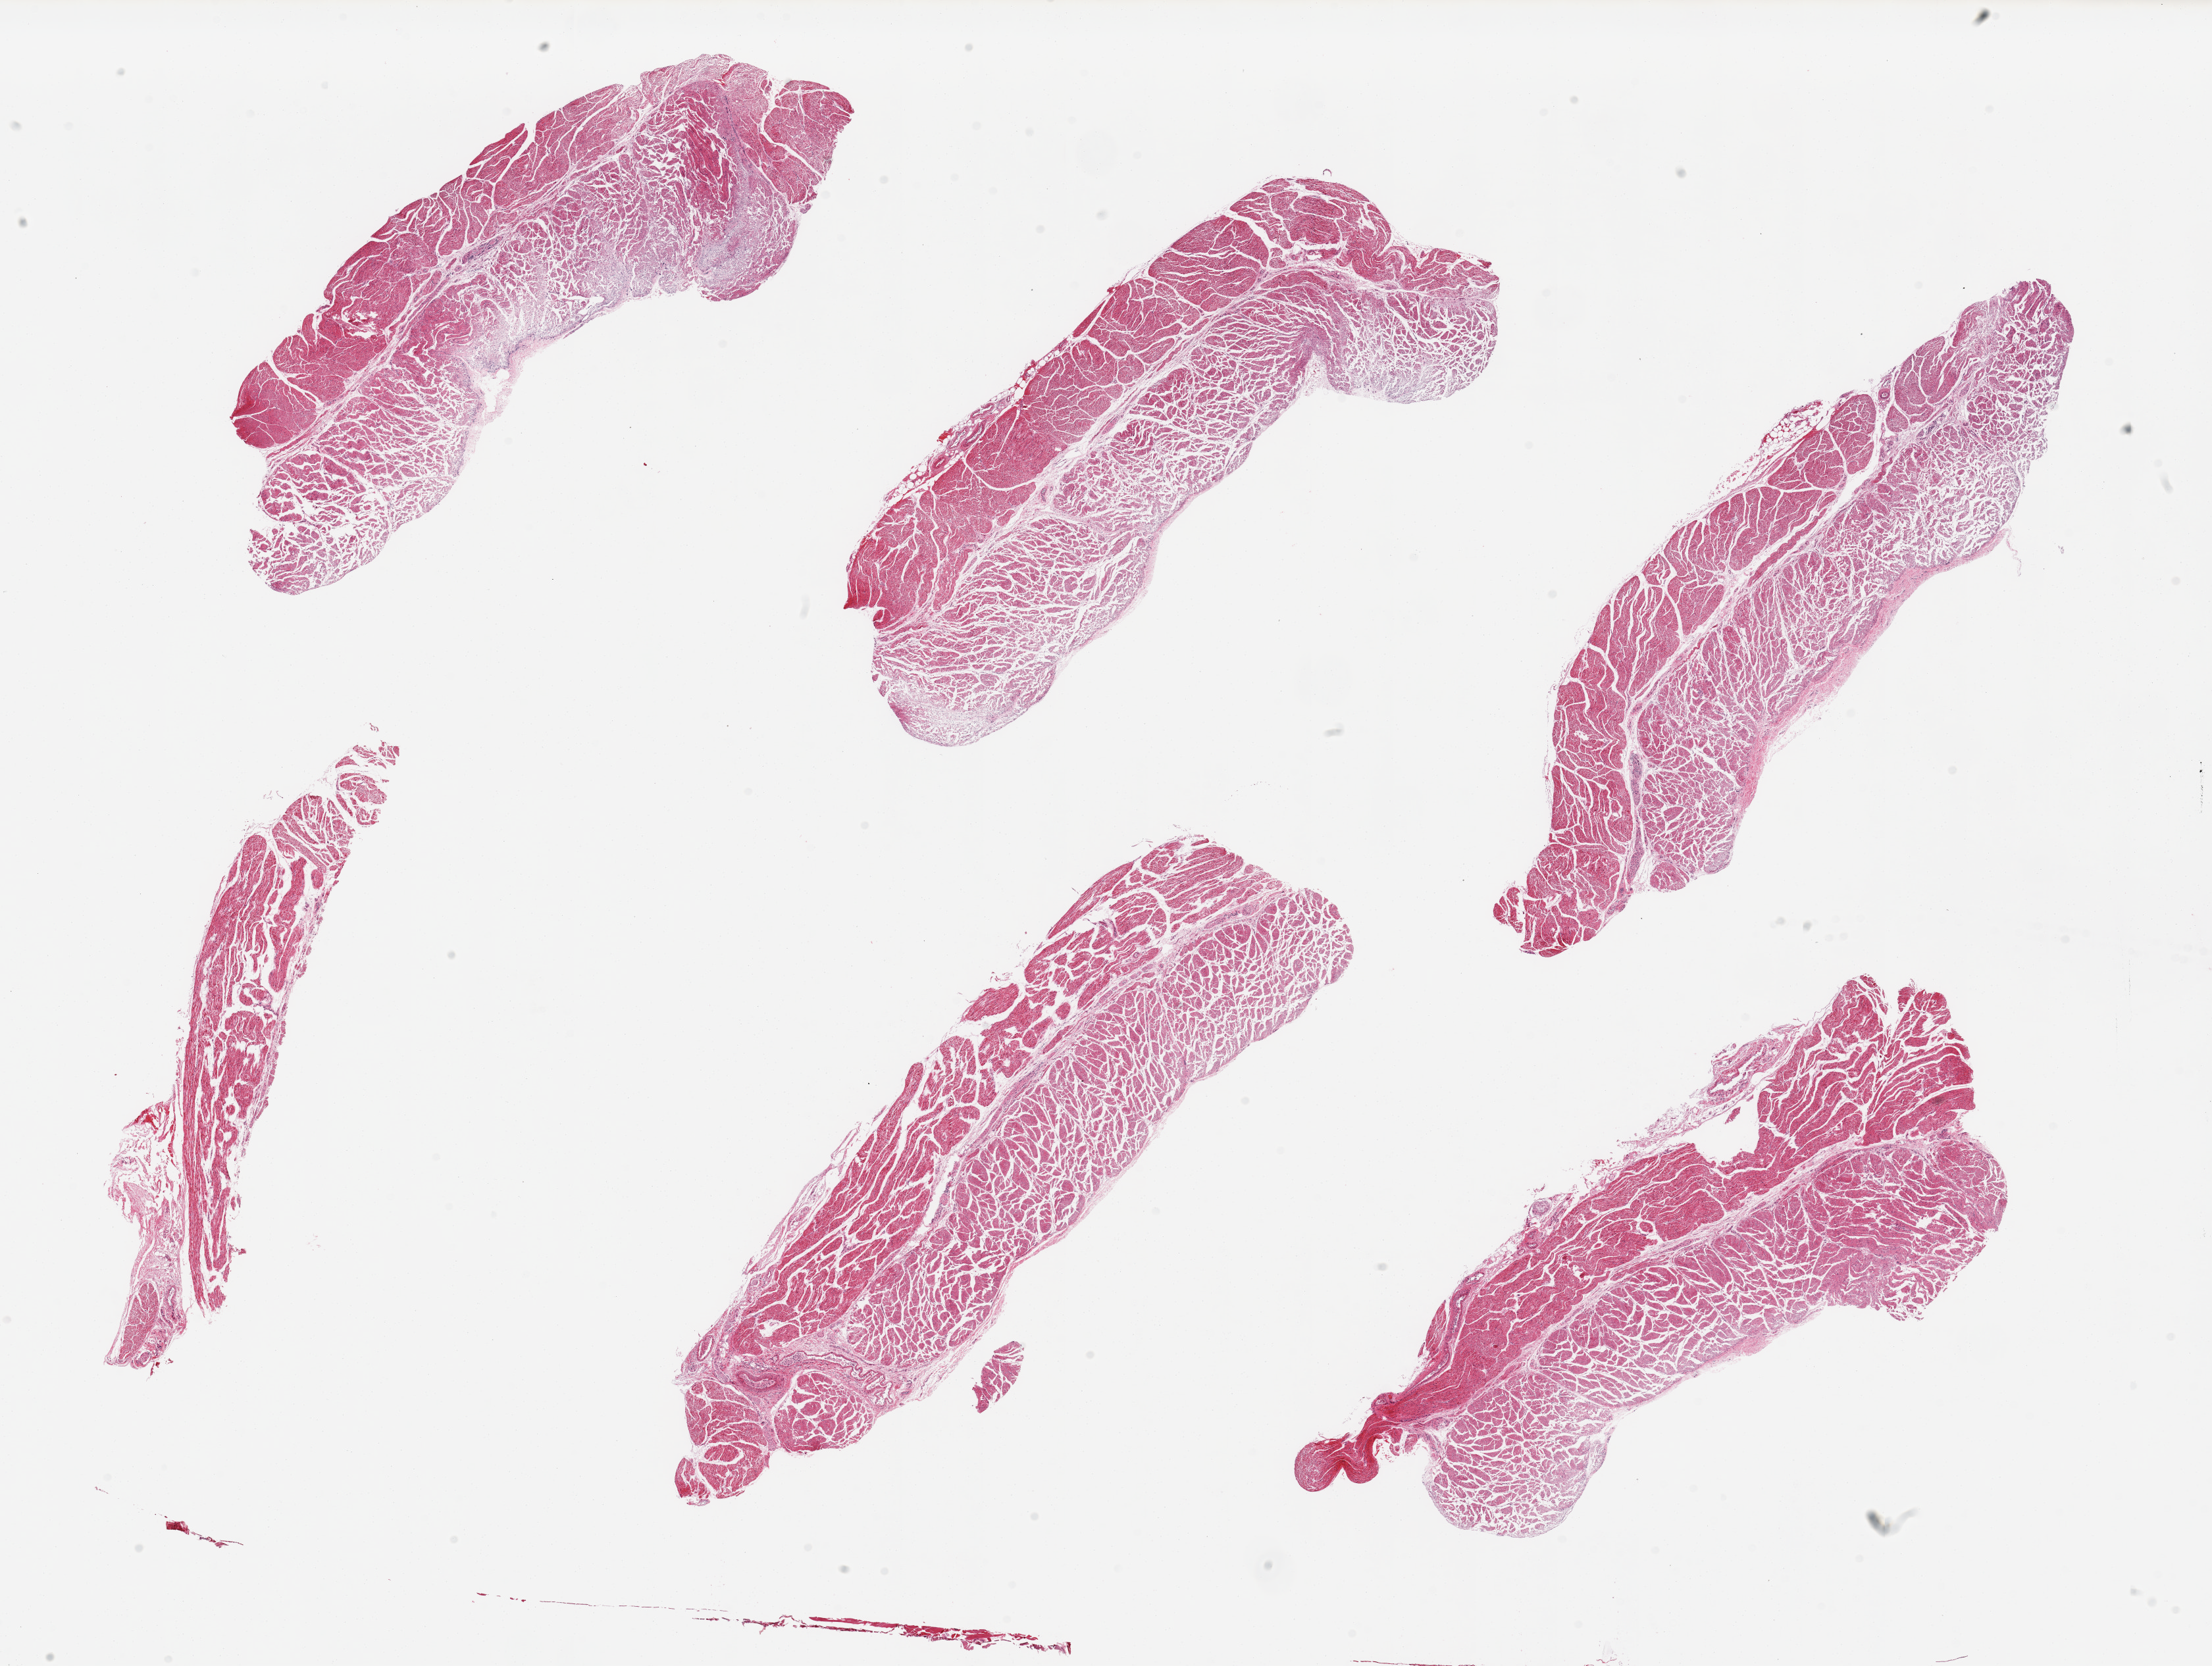
Whole-slide image, haematoxylin and eosin stain — low-resolution overview of the scanned area, about 26.6 x 20.0 mm (slide scanned at 20x); PAXgene-fixed paraffin-embedded (PFPE) section; target tissue: gastroesophageal junction; donor tissue sample. Donor sex: male.
* review note (as recorded): 6 pieces foci of unusual autolysis/necrosis